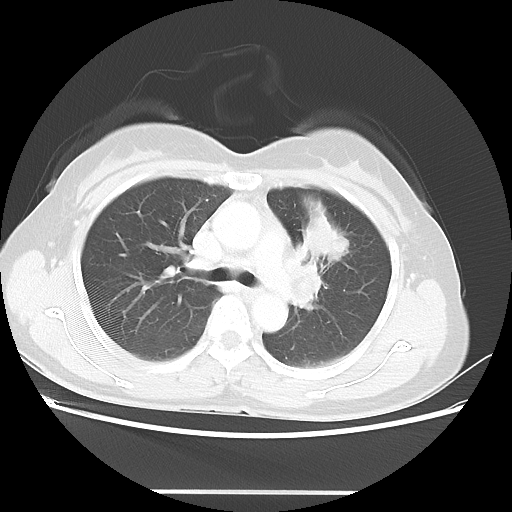
Chest CT, one axial slice; position 30 of 46 along the scan axis; reconstruction kernel LUNG; lung window (W 1500 / L -600 HU); 5 mm slice thickness; 512 × 512 image matrix, field of view 360 × 360 mm. Patient: female, 50 years. From the clinical record (not read from this slice): clinical TNM (as recorded): T1c N1 M0; histopathological grade: G3.
Structures marked on this image (rectangle marked by the reading radiologist):
- lung tumour (recorded histology: adenocarcinoma): bounding box [x1, y1, x2, y2] px = [304, 214, 349, 261]